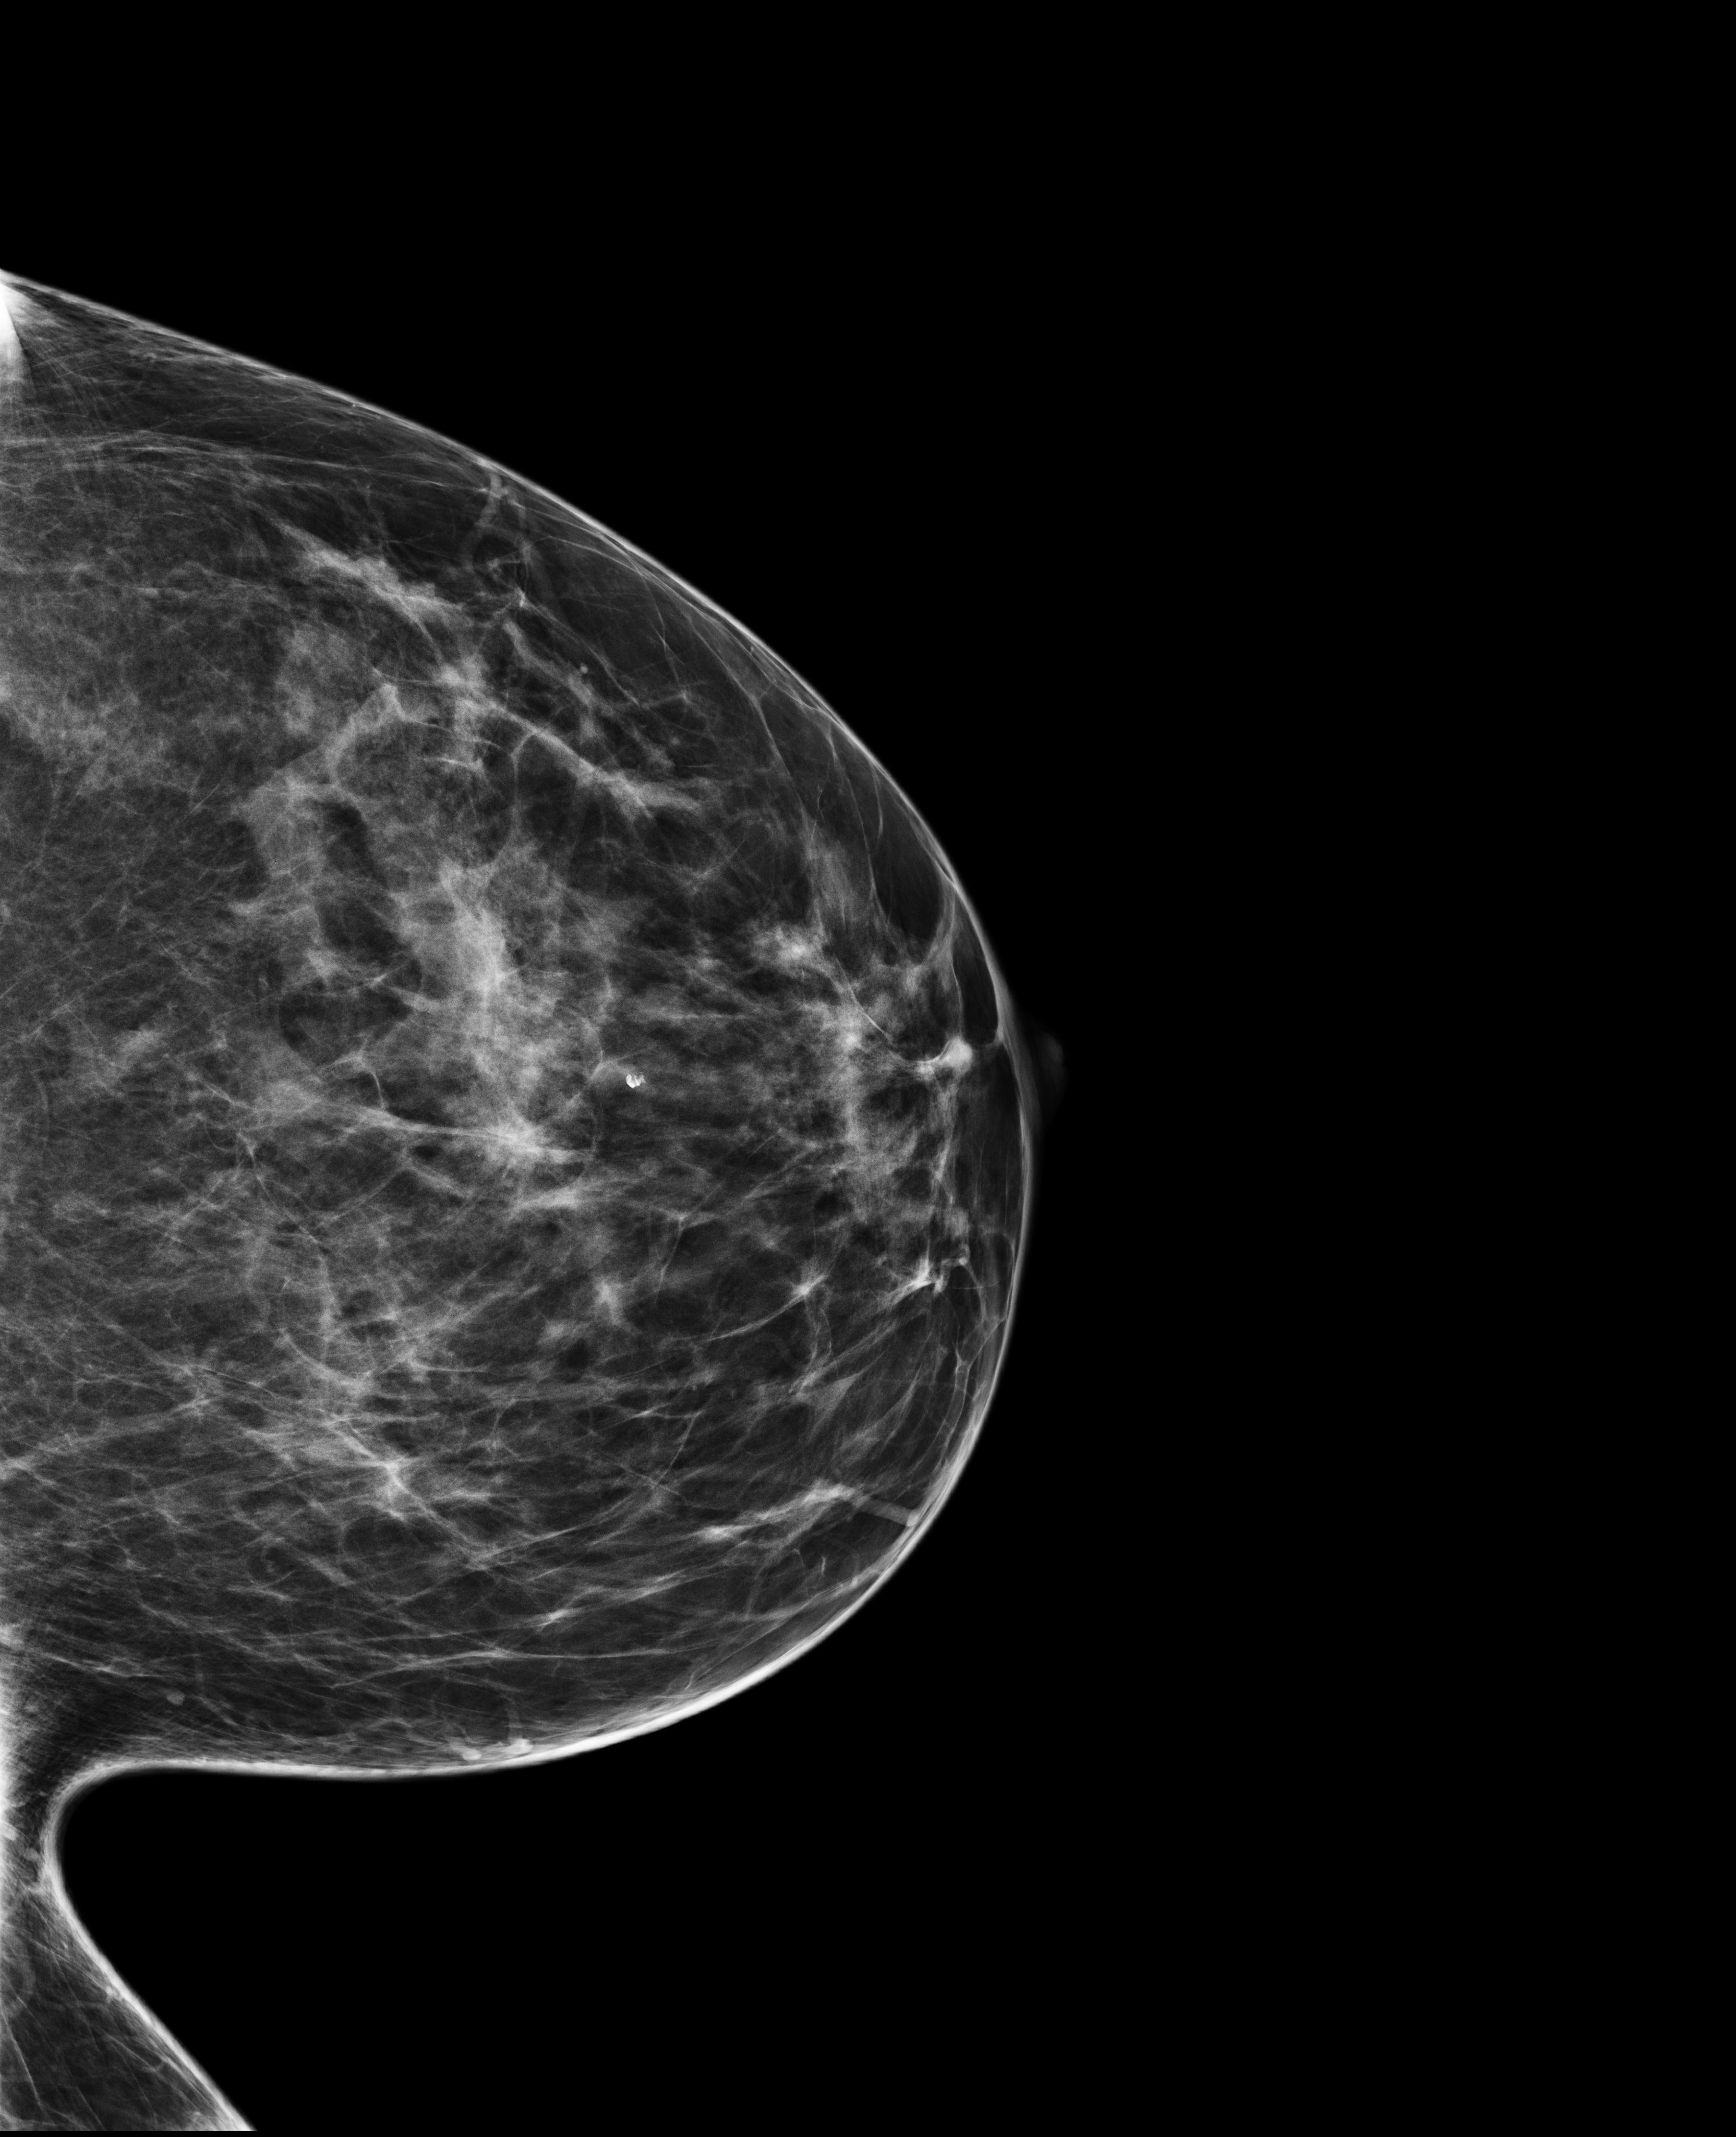
Full-field digital mammogram (FFDM), left breast, craniocaudal (CC) view, annual screening mammography examination, system: Selenia Dimensions. Patient: female, 47 years.
Breast density at the screening exam (both breasts): heterogeneously dense (BI-RADS density category c). Final BI-RADS assessment for this screening round (tomosynthesis exam, both breasts): category 2. Recall: no recall after this screen.